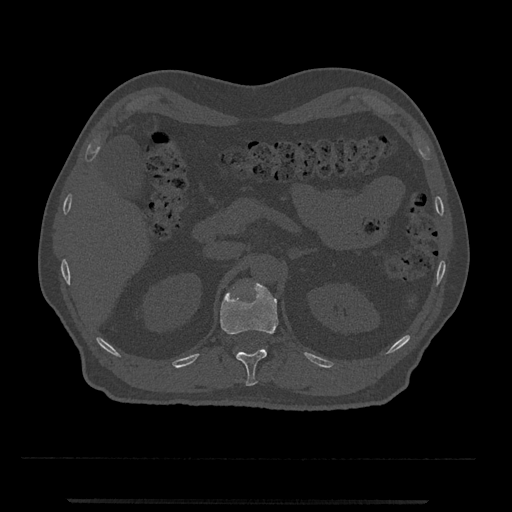
CT including the spine, one axial slice; slice 385 of 797 in the series (ordered by position); reconstruction kernel Br40s/3; bone window (W 1800 / L 400 HU); 0.5 mm slice thickness; 512 × 512 image matrix. Male patient, age 63 years. Case-level facts recorded for this patient, not image findings: primary cancer: prostate.
Structures marked on this image (semi-automatic segmentation, software-assisted and operator-edited):
- T12 vertebra: bounding box (x1, y1, x2, y2) in pixels: (220, 281, 278, 386)